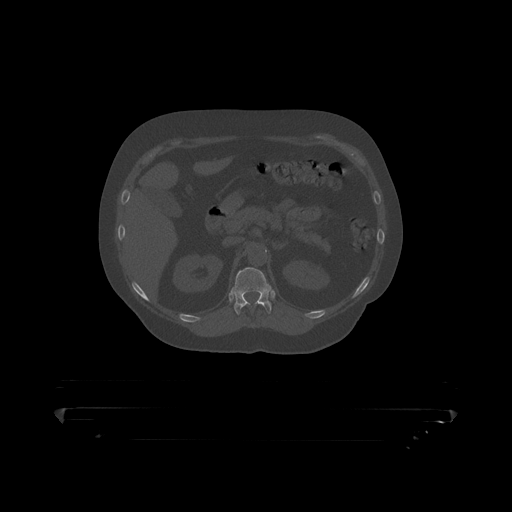
CT including the spine, one axial slice; position 177 of 390 along the scan axis; reconstruction kernel STANDARD; 120 kVp; bone window (W 1800 / L 400 HU); 1.25 mm slice thickness; 512 × 512 image matrix, field of view 650 × 650 mm. Patient: male, 60 years. From the clinical record (not read from this slice): primary cancer: prostate.
Structures marked on this image (semi-automatically segmented with operator editing):
- T12 vertebra: box from (x=232, y=268) to (x=272, y=316) px